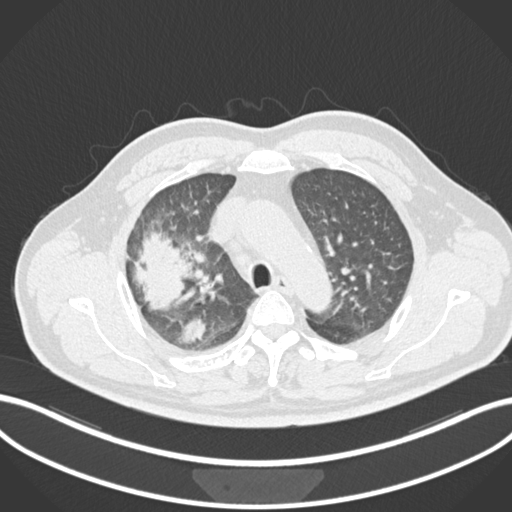
Chest CT, one axial slice. Slice 671 of 852 in the series (ordered by position). Reconstruction kernel B30f. 120 kVp. Lung window (W 1500 / L -600 HU). 512 × 512 image matrix. Patient: male, 55 years. Case-level facts recorded for this patient, not image findings: clinical TNM (as recorded): T3 N2 M1.
Outlined on this slice (bounding box drawn by a radiologist):
- lung tumour (recorded histology: adenocarcinoma): box from (x=131, y=230) to (x=199, y=314) px